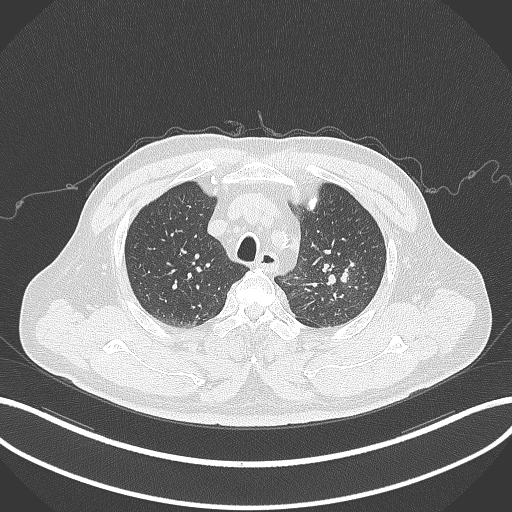
Chest CT, one axial slice. 120 kVp. Lung window (W 1500 / L -600 HU). 1 mm slice thickness. 512 × 512 image matrix, field of view 400 × 400 mm. Male patient, age 67 years. Case-level facts recorded for this patient, not image findings: clinical TNM (as recorded): T2a N1 M0.
Annotated regions visible in this slice (rectangle marked by the reading radiologist):
- lung tumour (recorded histology: adenocarcinoma): bounding box (x1, y1, x2, y2) in pixels: (317, 258, 353, 286)